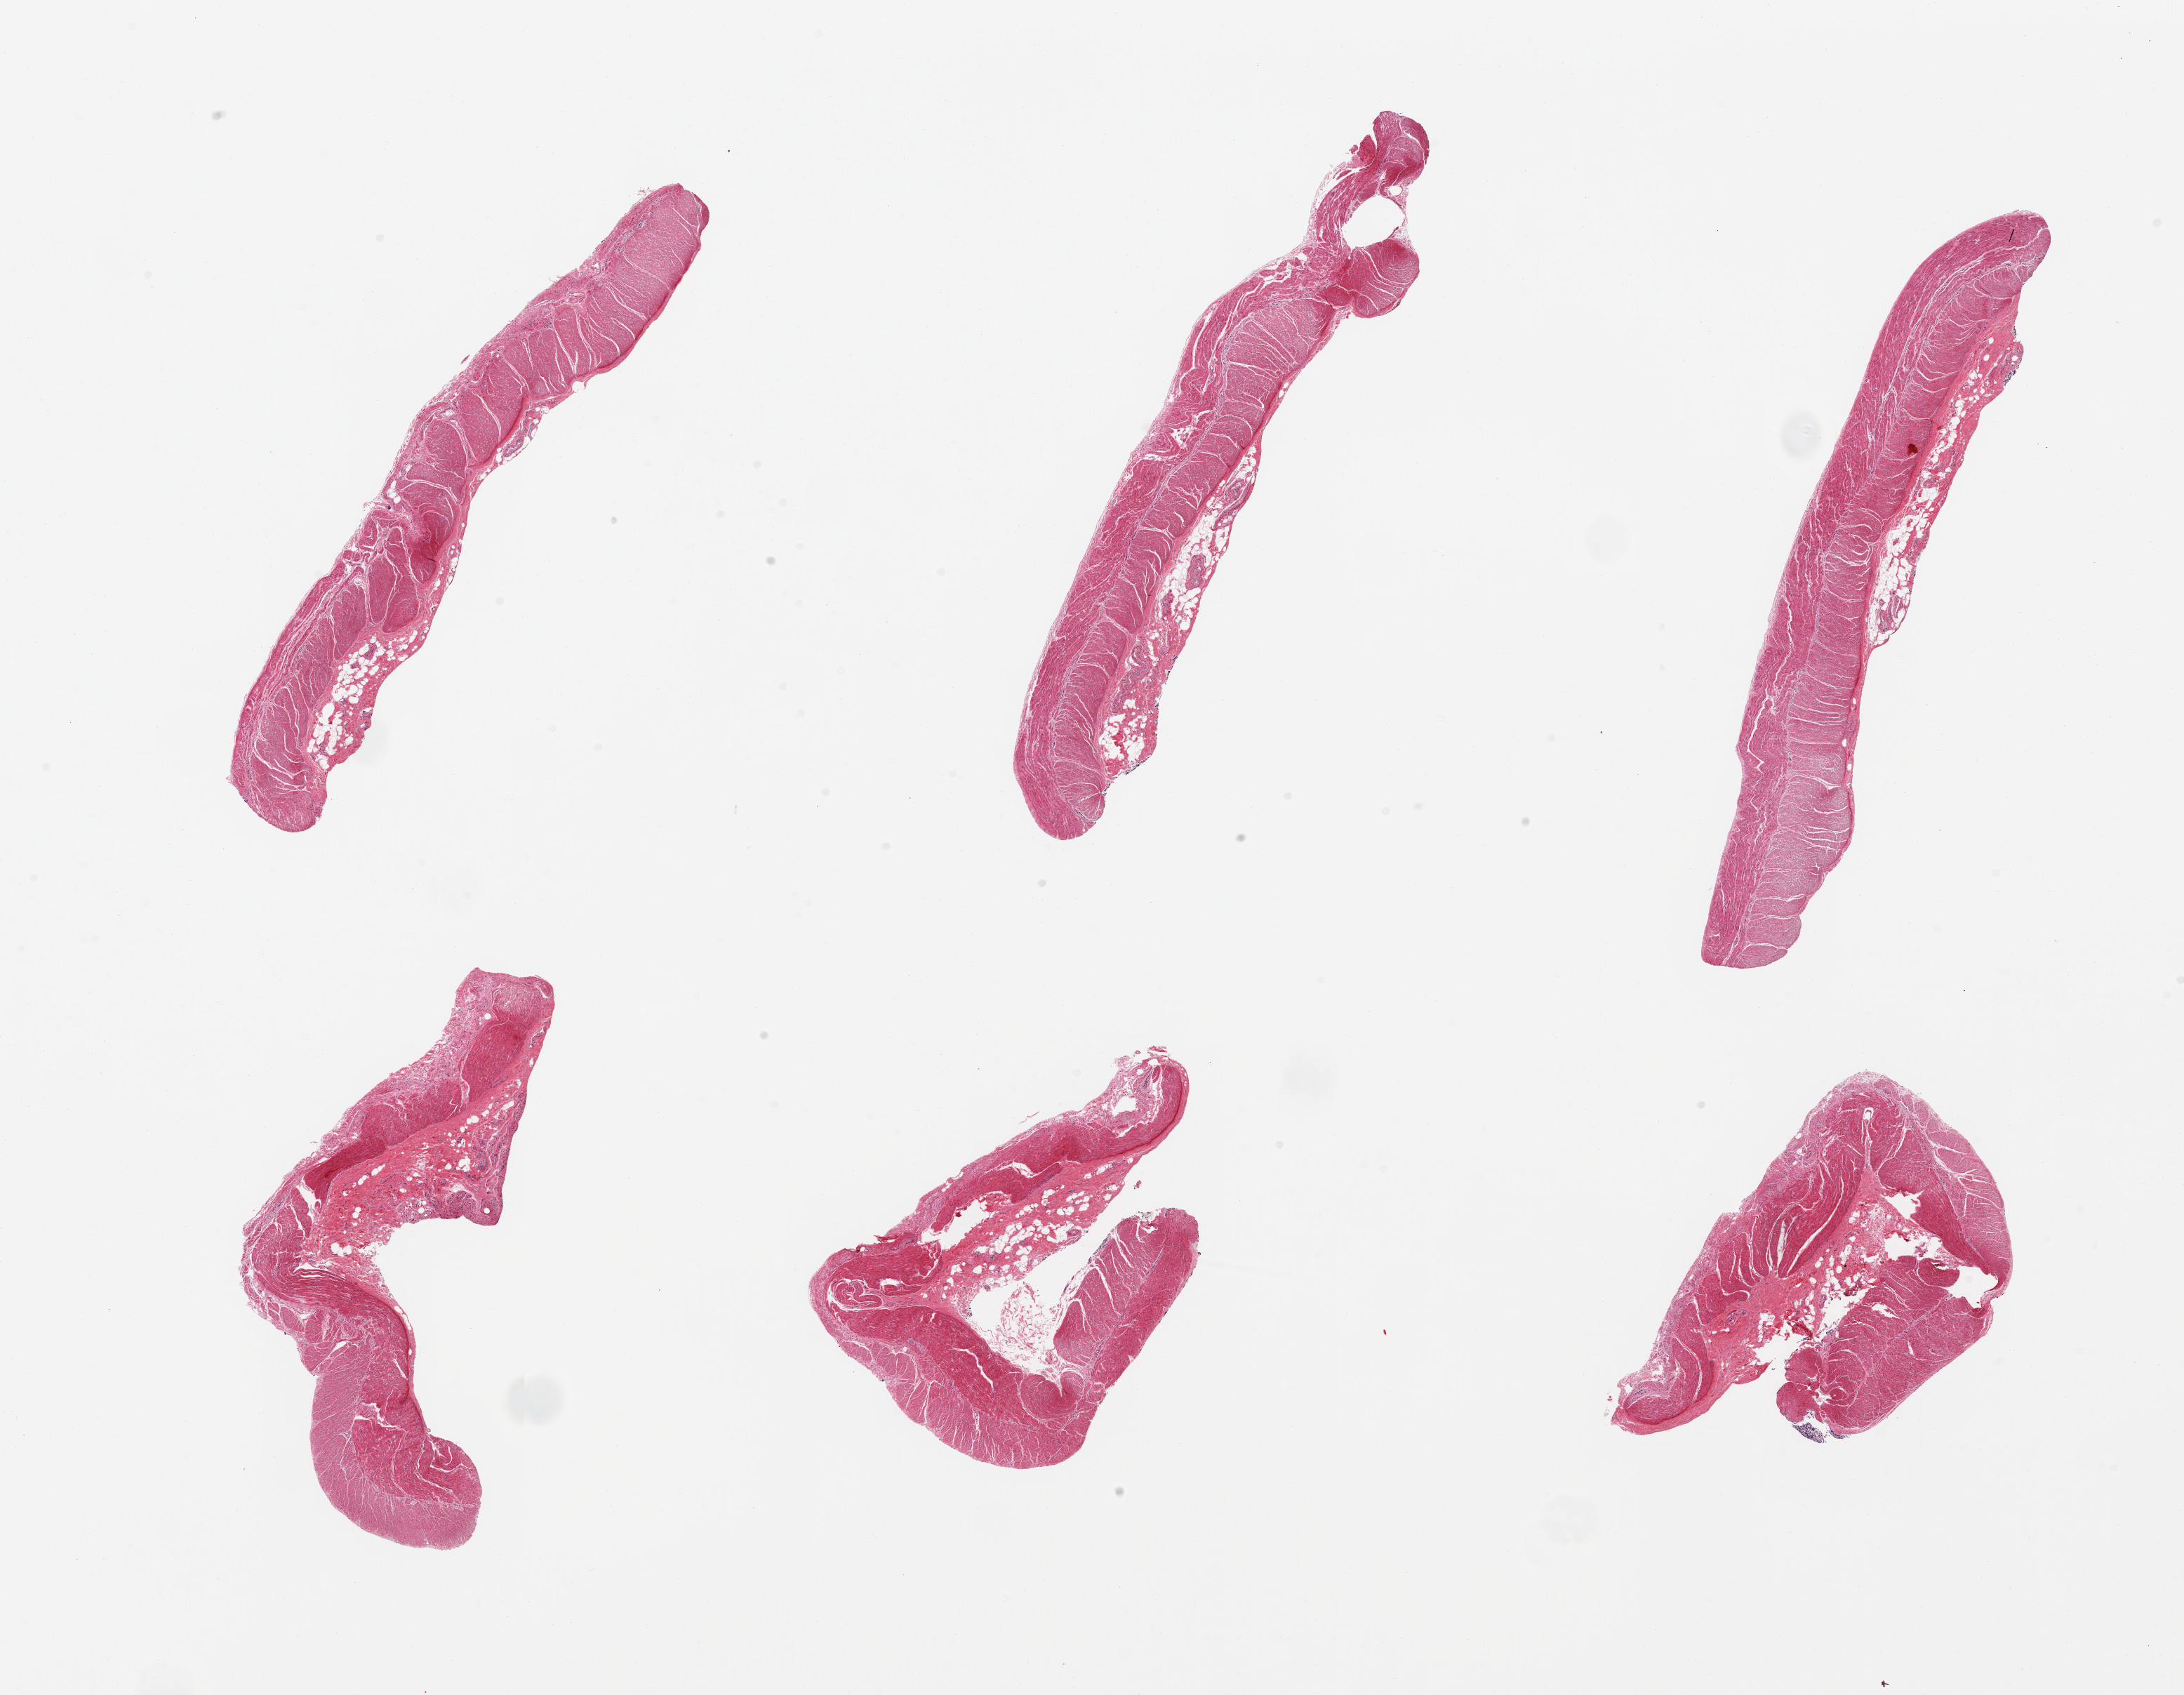
Hematoxylin and eosin (H&E) whole-slide image, brightfield, shown as a low-resolution overview of the whole scanned area (about 24.6 x 19.1 mm). PAXgene-fixed, paraffin-embedded tissue. Section of sigmoid colon (target tissue). Tissue donor sample. Donor sex: male.
- reviewer comment on this tissue sample: 6 pieces; target muscularis and attached fibrovascular tissue up to 0.6mm